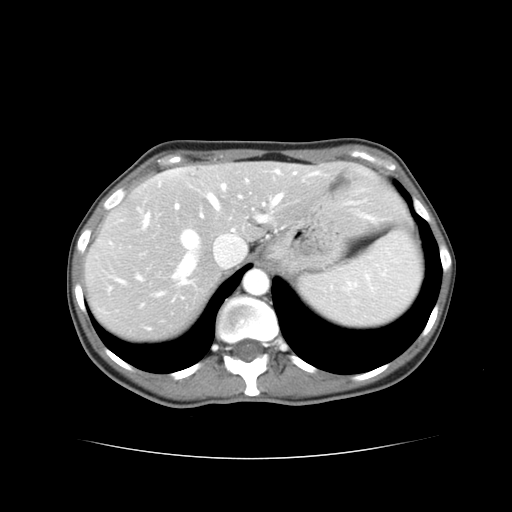
Contrast-enhanced abdominal CT, one axial slice. Slice 30 of 38 in the series (ordered by position). Intravenous contrast given. Soft-tissue window (W 400 / L 40 HU). 5 mm slice thickness. 512 × 512 image matrix. Female patient, age 54 years. From the clinical record (not read from this slice): diagnosis: colorectal cancer liver metastases, imaged before liver resection; multiple liver metastases: yes; largest metastasis: 1.1 cm; chemotherapy before resection: yes.
Annotated regions visible in this slice (outlined manually by an expert reader):
- hepatic veins: bounding box <174,195,282,284> (left, top, right, bottom; pixels)
- liver: <87,165,402,338>
- planned liver remnant (the part of the liver to remain after resection): <208,165,403,239>
- portal vein (with intrahepatic branches): <140,196,267,281>
- liver metastasis: <329,175,352,192>